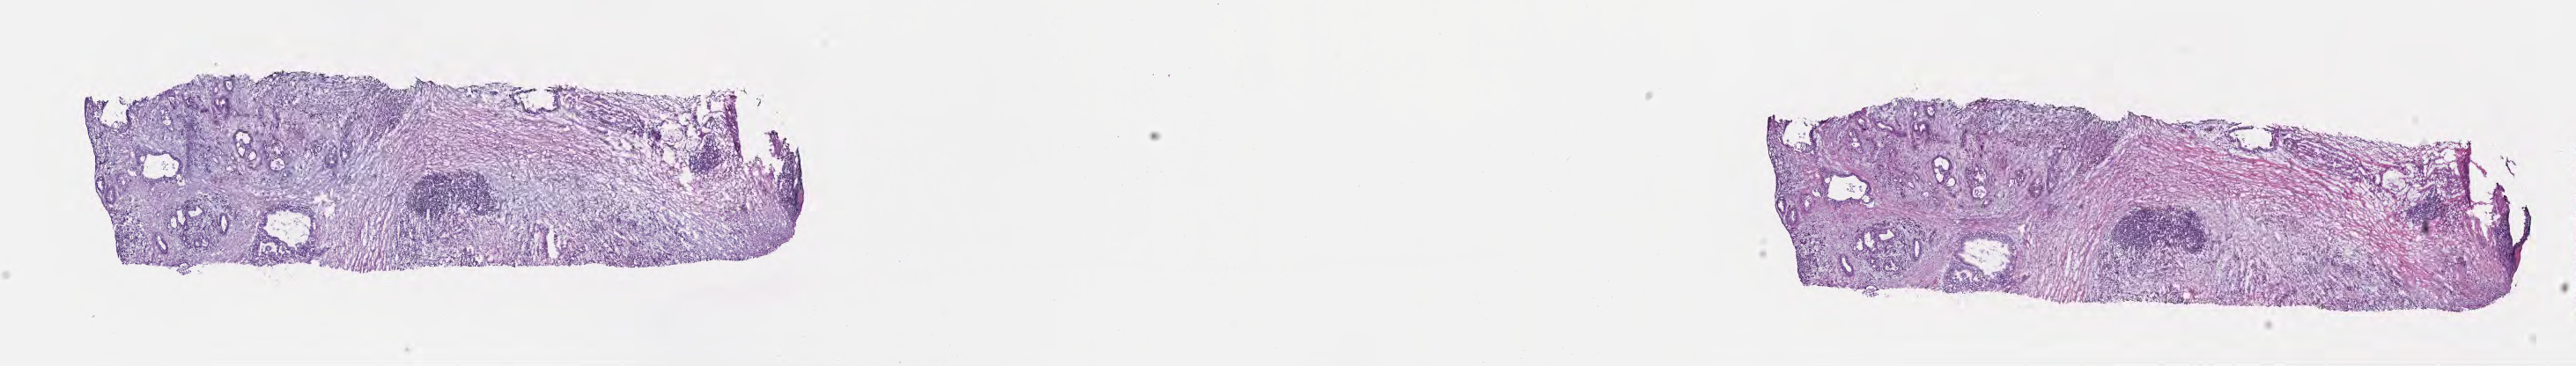
H&E whole-slide image, low-resolution overview of the scanned area, about 23.6 x 3.4 mm, frozen section (tissue freezing medium), primary tumor, site: head of pancreas. Male, age 53 years at initial diagnosis. Slide review estimates, as recorded: tumor cells 22%, tumor nuclei 35%, stromal cells 77%, necrosis 1%, normal cells 0%. Inflammatory infiltration, as recorded: lymphocyte infiltration 50%, monocyte infiltration 2%, neutrophil infiltration 0%.
Histologic diagnosis: Infiltrating duct carcinoma, NOS.